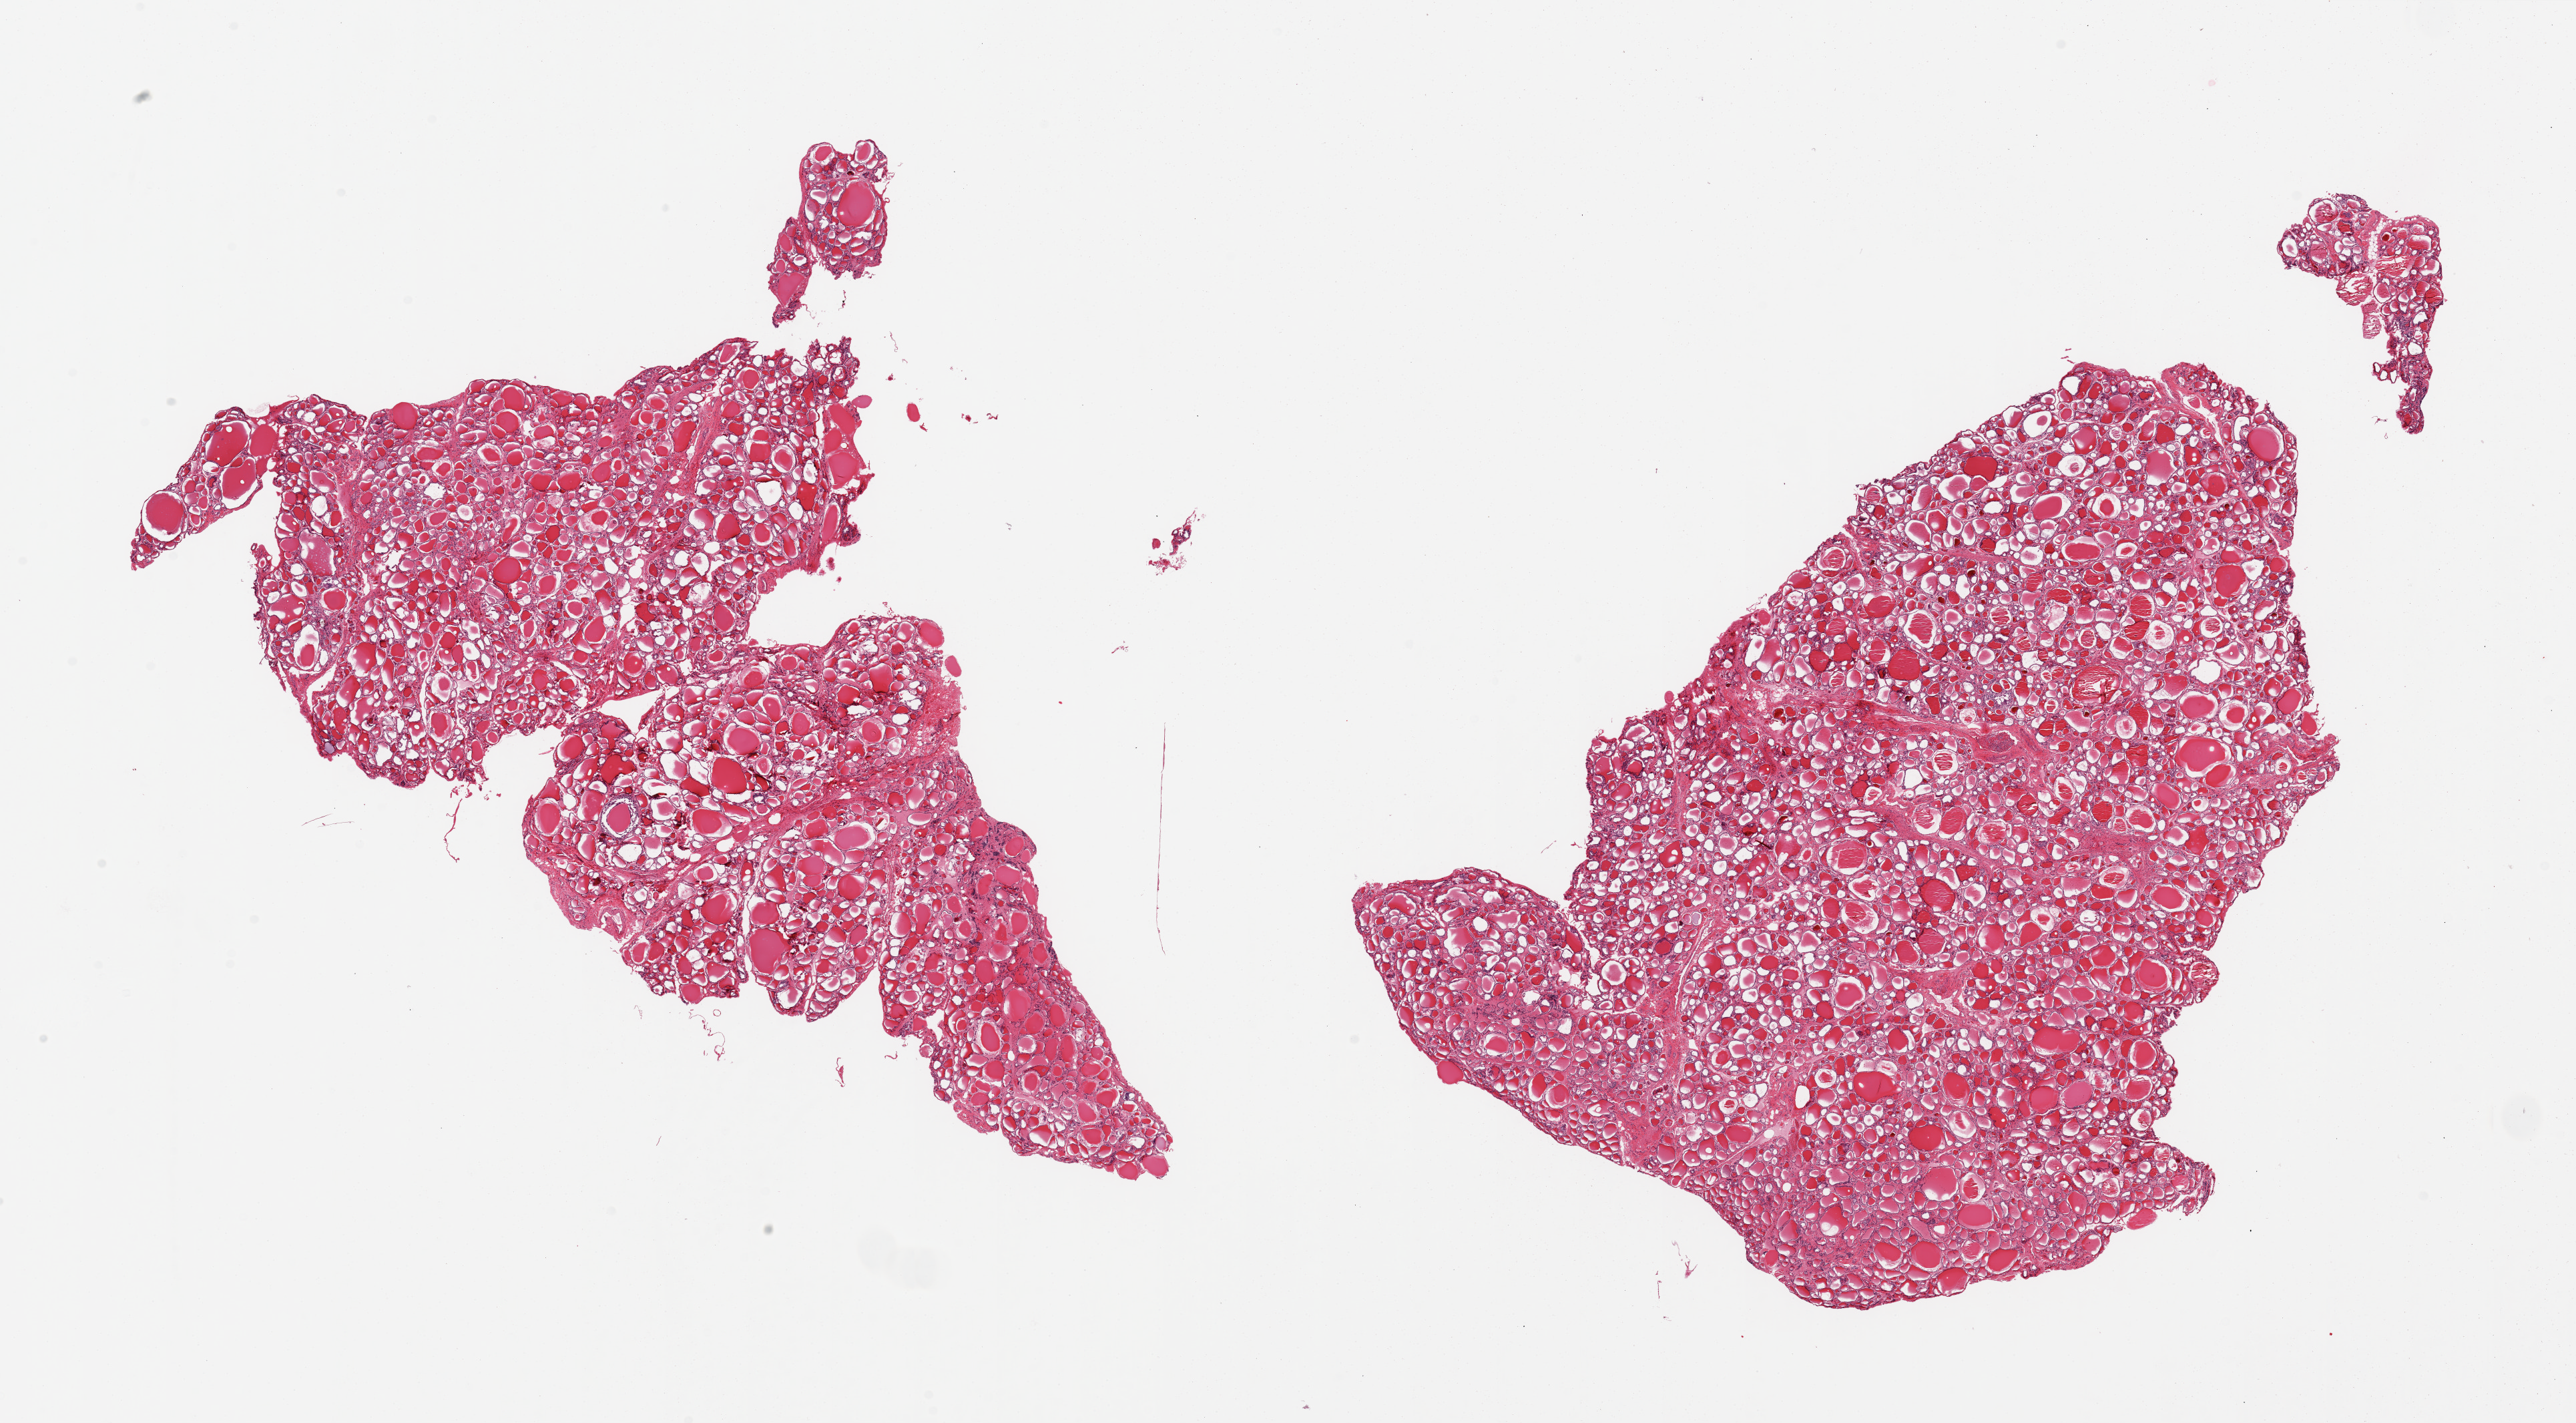
Digitized haematoxylin and eosin-stained section — a low-resolution overview of the entire scanned area, about 30.5 x 16.9 mm (from a 20x scan); PAXgene-fixed paraffin-embedded (PFPE) section; target tissue: thyroid; tissue donor sample. Donor: female.
Pathologist's review note for this sample: 2 pieces, well preserved, minimal inflammation.